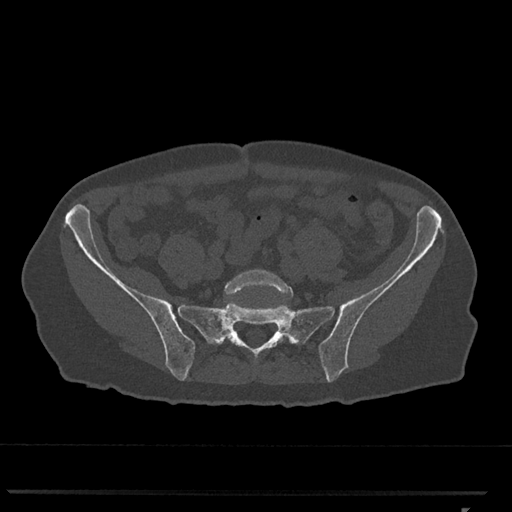
CT including the spine, one axial slice; slice 114 of 793 in the series (ordered by position); reconstruction kernel Br40s/3; 120 kVp; bone window (W 1800 / L 400 HU); 0.5 mm slice thickness; 512 × 512 image matrix. Female patient, age 62 years. Case-level facts recorded for this patient, not image findings: primary cancer: renal.
Structures marked on this image (semi-automatic segmentation, software-assisted and operator-edited):
- L5 vertebra: bounding box <224,269,294,340> (left, top, right, bottom; pixels)